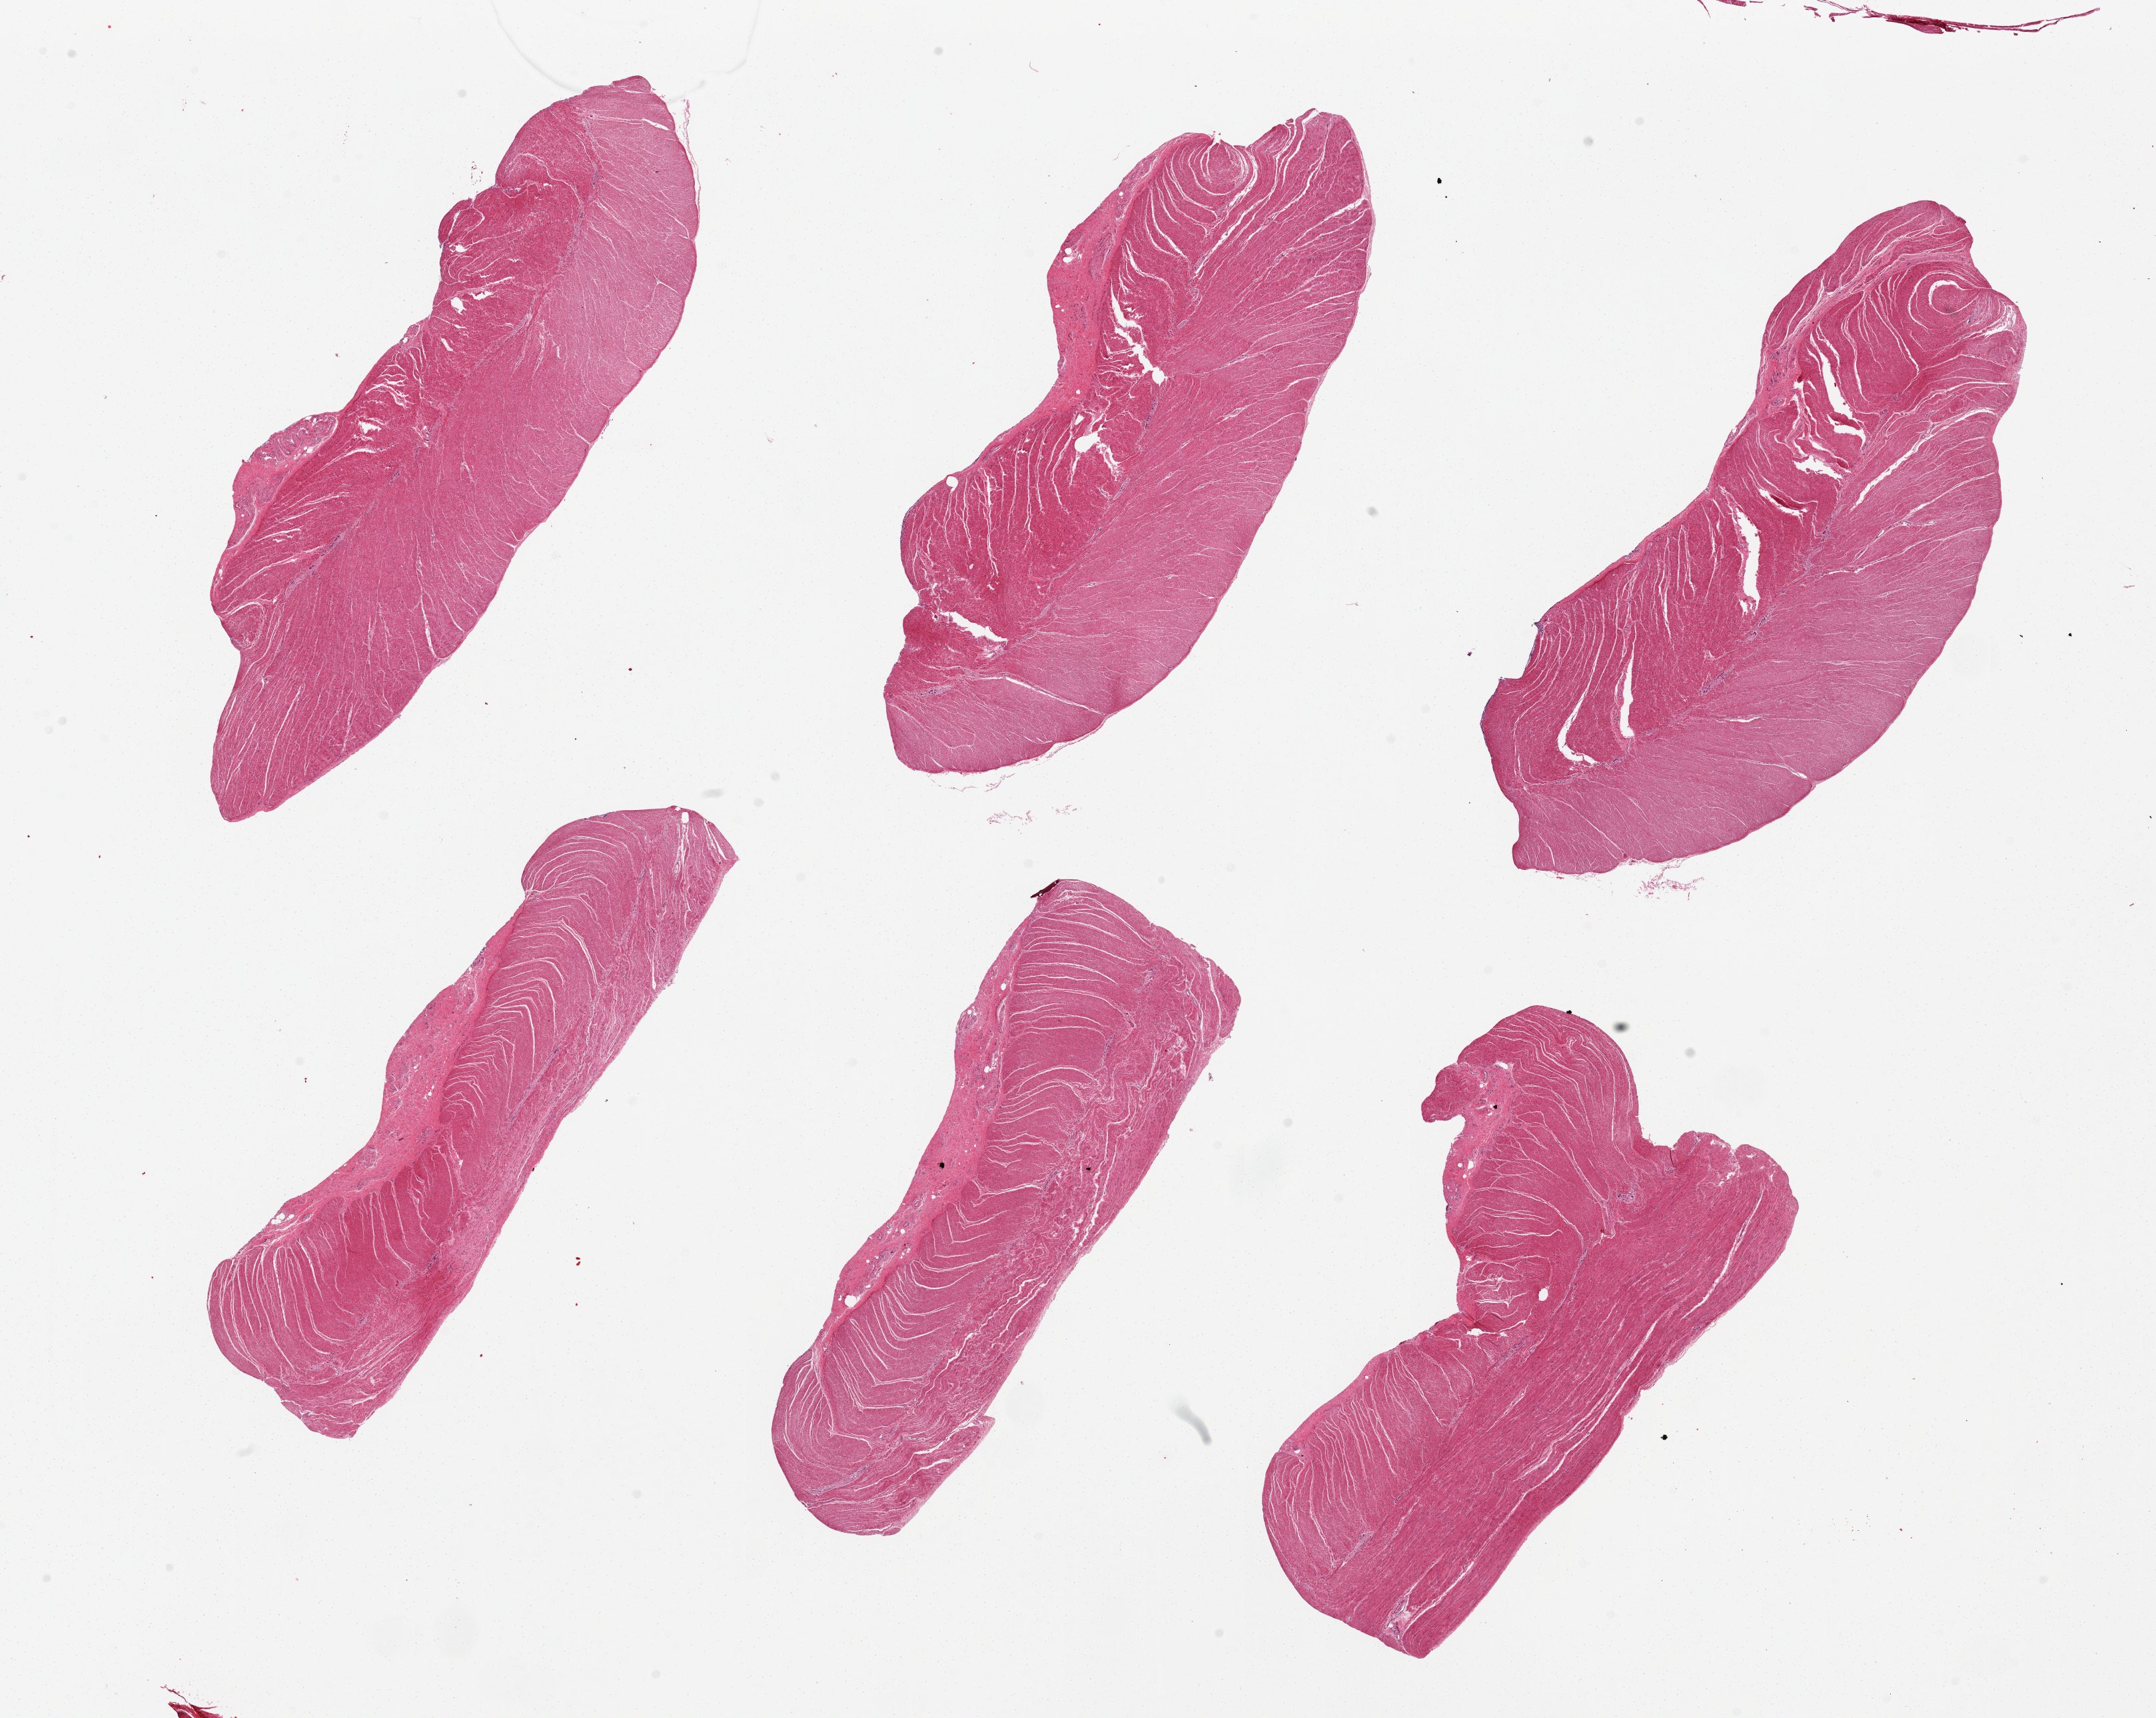
Digitized hematoxylin and eosin (H&E)-stained section — a low-resolution overview of the entire scanned area, about 25.6 x 20.4 mm. PAXgene-fixed paraffin-embedded (PFPE) section. Section of sigmoid colon (target tissue). Tissue donor sample. Donor sex: male.
Pathologist's review note for this sample: 6 pieces, all muscularis propria, appropriate good specimens.